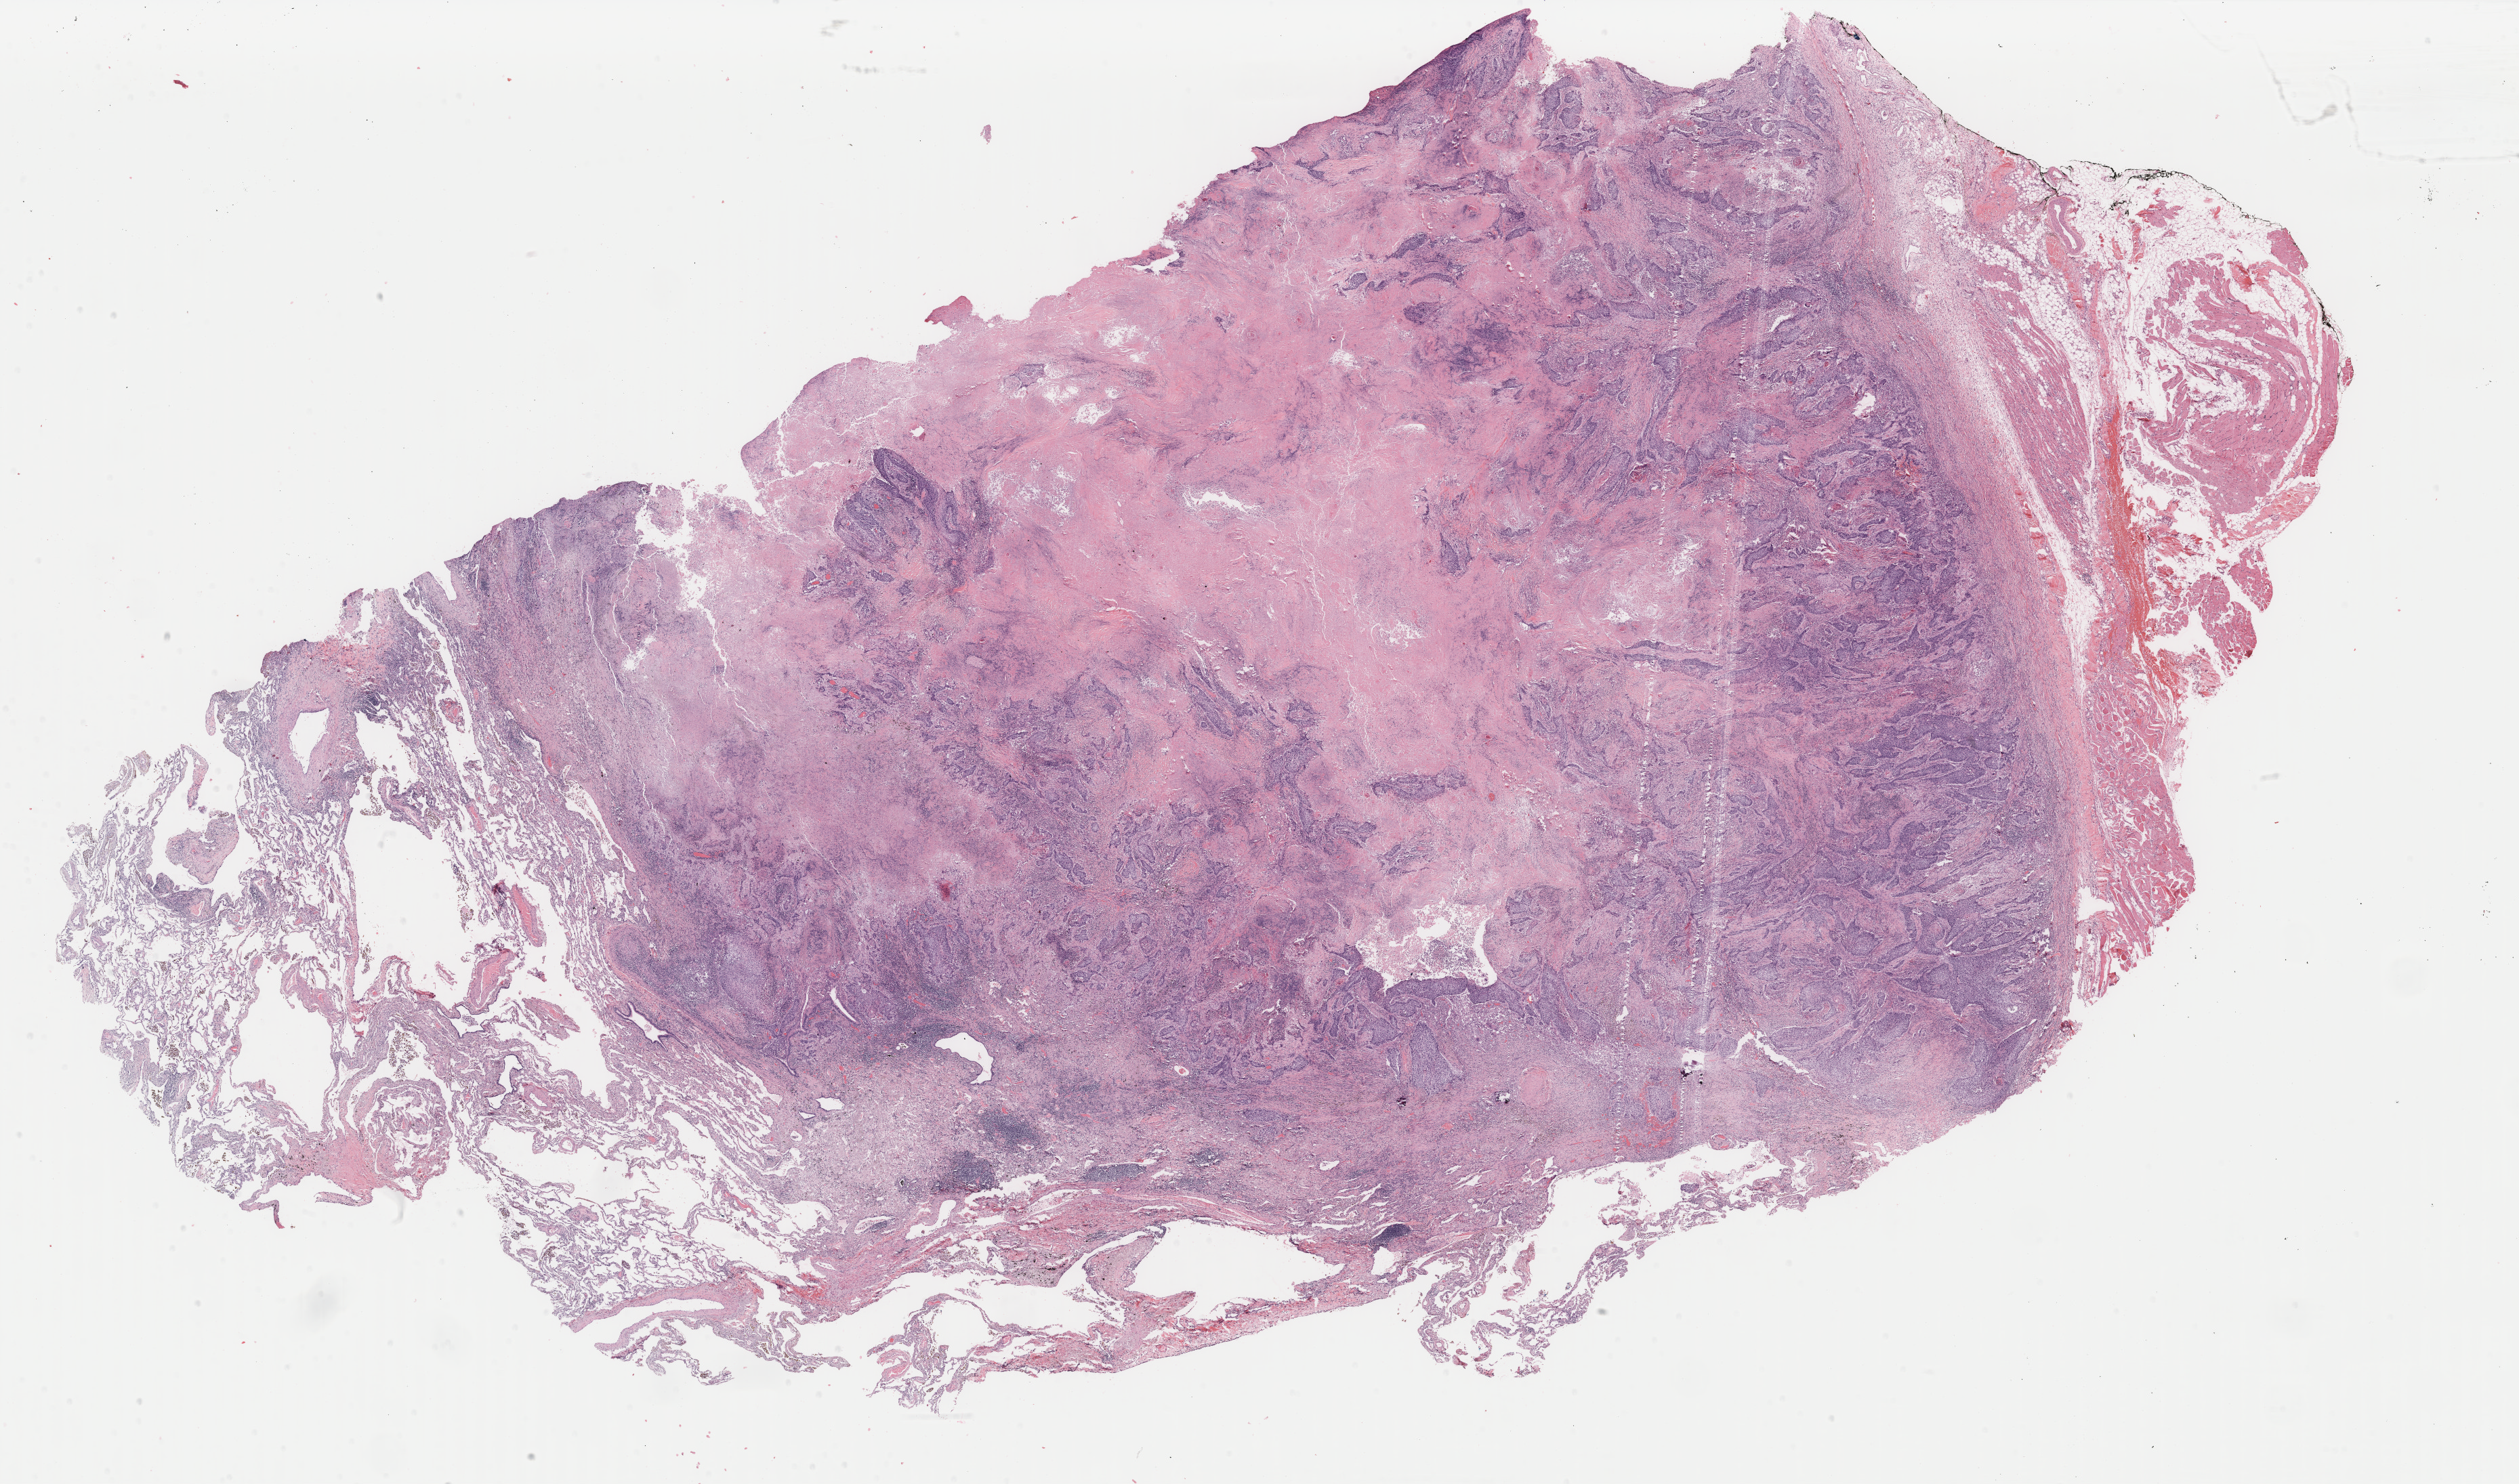
Whole-slide histology image, H&E — shown as a low-resolution overview of the whole scanned area (about 29.5 x 17.4 mm), FFPE section, lung, primary tumour sample. Male patient; age at initial diagnosis 70 years.
AJCC pathologic stage: IIB (6th edition). Histologic diagnosis: Squamous cell carcinoma, NOS (upper lobe, lung).